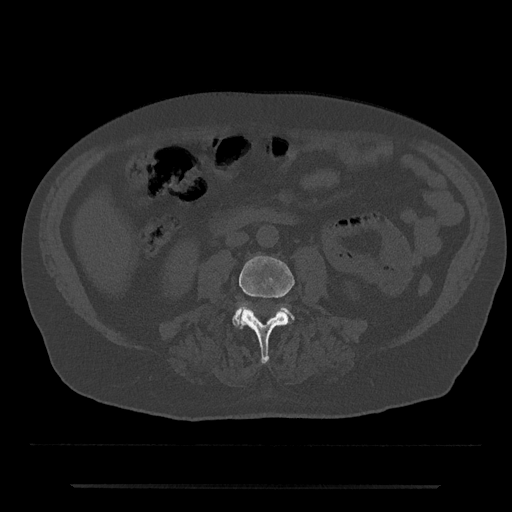
CT including the spine, one axial slice. Position 395 of 797 along the scan axis. Bone window (W 1800 / L 400 HU). 0.5 mm slice thickness. 512 × 512 image matrix. Male patient, age 80 years. Case-level facts recorded for this patient, not image findings: primary cancer: prostate; vertebrae with lytic lesions (as recorded): L1, T11.
Annotated regions visible in this slice (semi-automatically segmented with operator editing):
- L3 vertebra: box from (x=238, y=256) to (x=295, y=364) px
- L4 vertebra: (x=232, y=305)–(x=294, y=327)